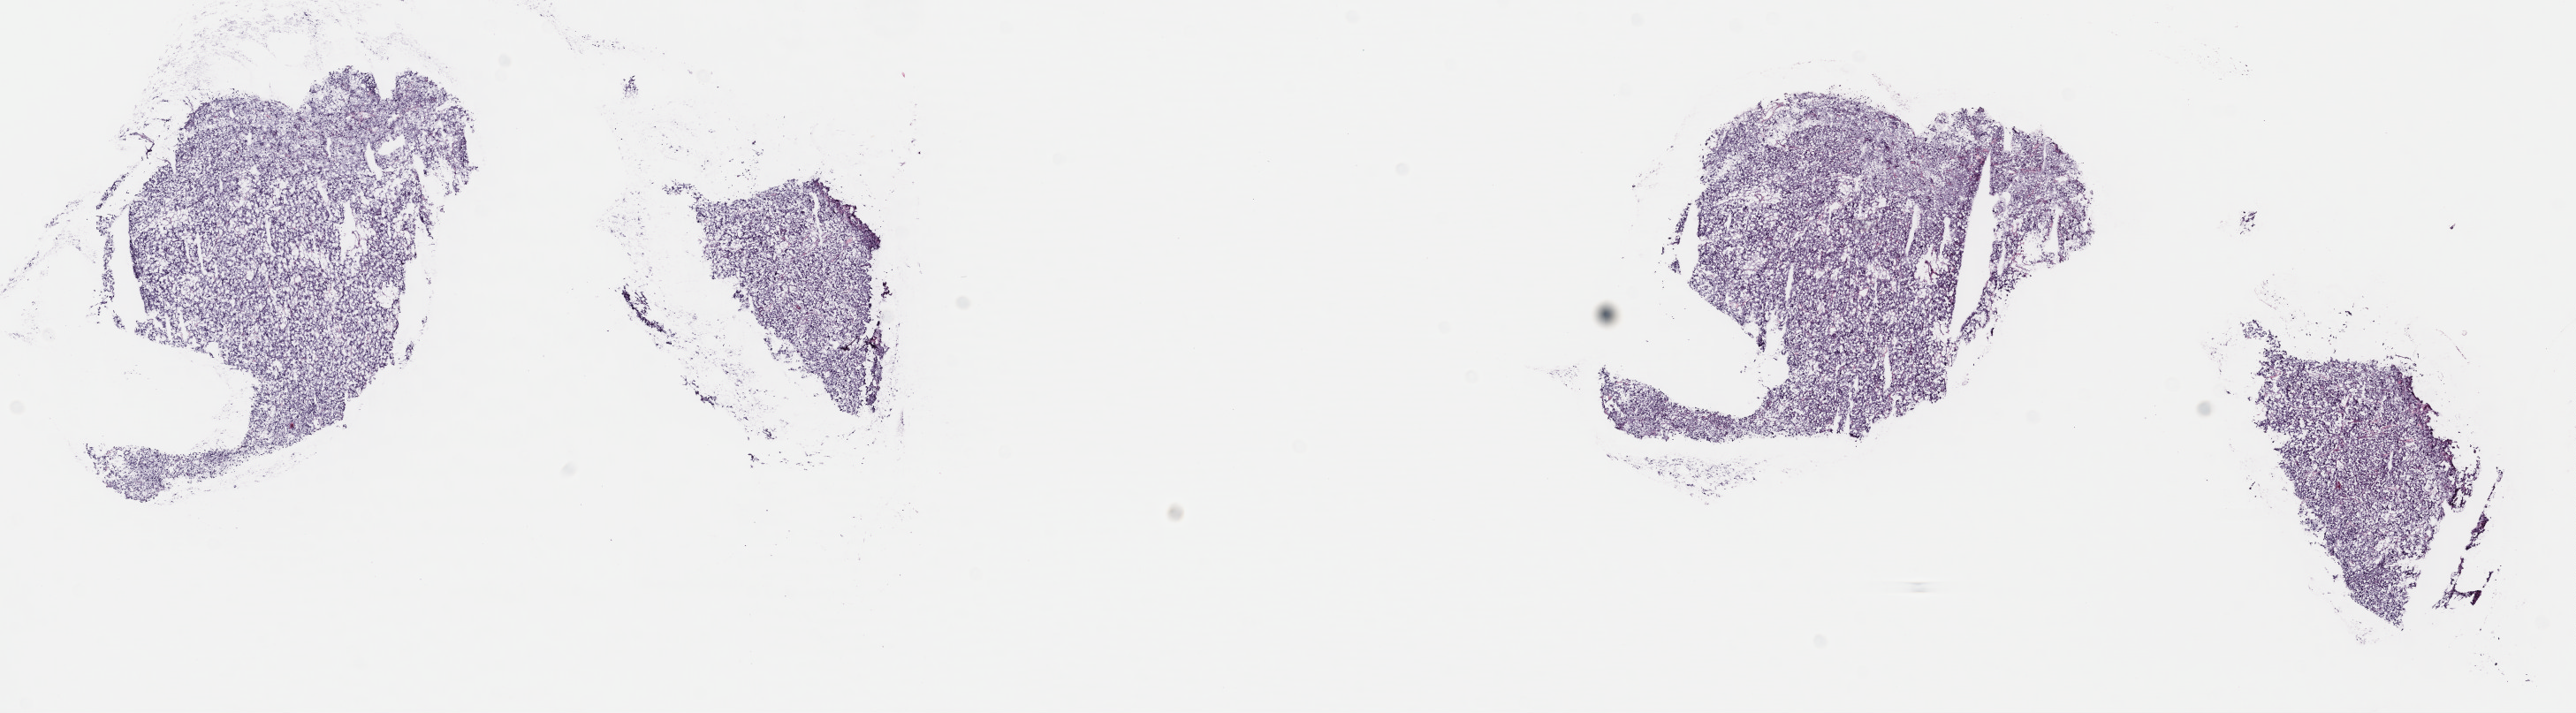
Digitized Hematoxylin and eosin (H&E) stained tissue section (whole slide) — a low-resolution overview of the entire scanned area, about 22.9 x 6.3 mm (from a 40x scan), frozen section from the top of the tissue portion, metastatic tumour sample. Patient: male, age at initial diagnosis 62 years. Slide review estimates, as recorded: tumour cells 95%, tumour nuclei 95%, normal cells 0%, stromal cells 5%, necrosis 0%. Inflammatory infiltration, as recorded: lymphocyte infiltration 0%, monocyte infiltration 0%, neutrophil infiltration 0%.
* this section: metastatic tumour tissue
* patient diagnosis: Pheochromocytoma, malignant